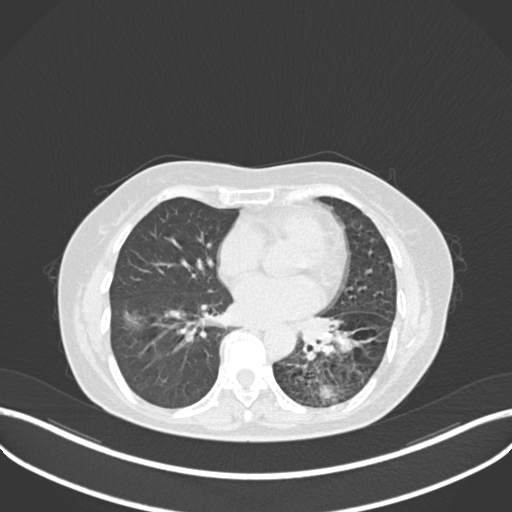
Chest CT, one axial slice; slice 112 of 270 in the series (ordered by position); reconstruction kernel B30f; 120 kVp; lung window (W 1500 / L -600 HU); 1 mm slice thickness; 512 × 512 image matrix, field of view 400 × 400 mm. Patient: female, 63 years. Case-level facts recorded for this patient, not image findings: clinical TNM (as recorded): T1b N0 M0.
Outlined on this slice (bounding box drawn by a radiologist):
- lung tumour (recorded histology: adenocarcinoma): box from (x=295, y=310) to (x=360, y=358) px